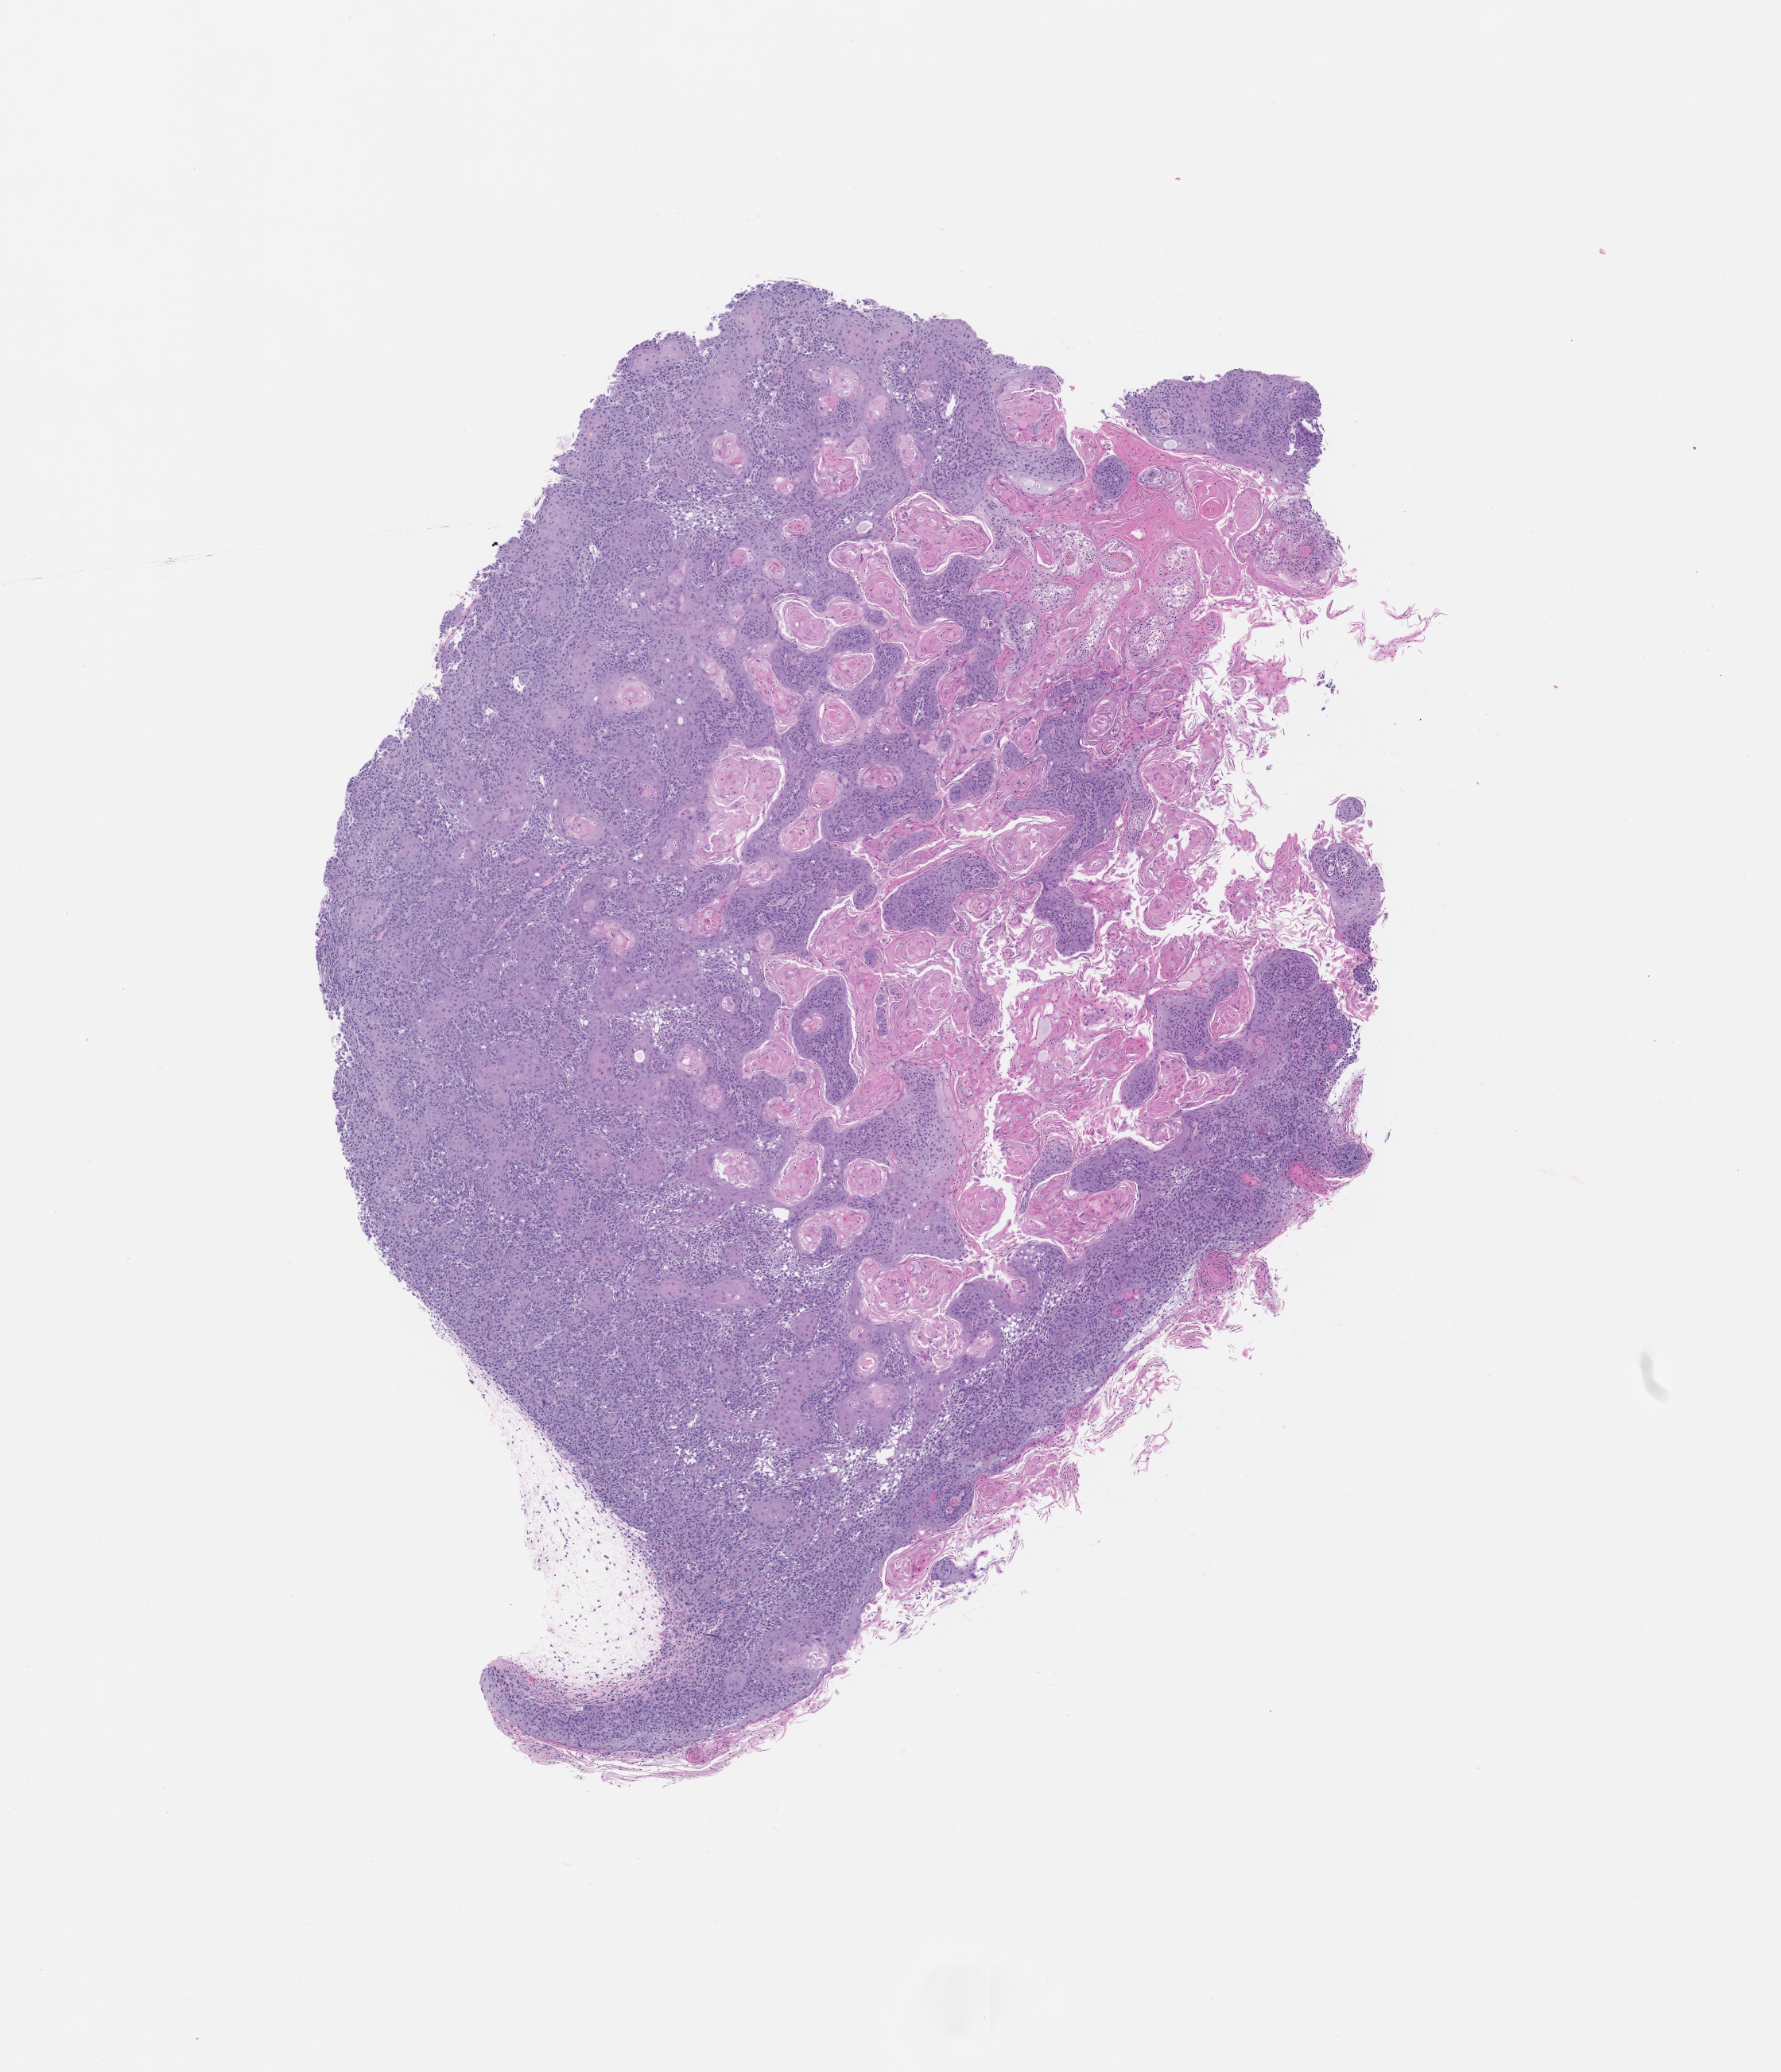
Hematoxylin and eosin (H&E) whole-slide image of a patient-derived xenograft (PDX) tumor grown in a mouse, passage 0 — whole scanned area (about 9.0 x 10.4 mm) shown as a low-resolution overview, formalin-fixed, paraffin-embedded (FFPE) tissue, originating tumor site category: oral soft tissue.
Originating patient diagnosis: Head and Neck Squamous Cell Carcinoma.